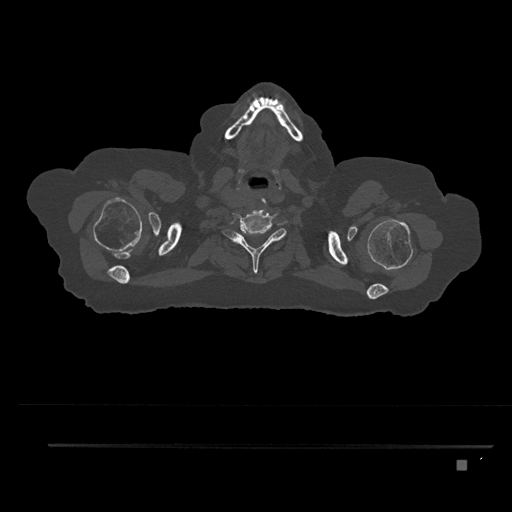
CT including the spine, one axial slice. Position 731 of 797 along the scan axis. Reconstruction kernel Br40s/3. 120 kVp. Bone window (W 1800 / L 400 HU). 0.5 mm slice thickness. 512 × 512 image matrix, field of view 437 × 437 mm. Female patient, age 76 years. Case-level facts recorded for this patient, not image findings: primary cancer: lung; vertebrae with lytic lesions (as recorded): T11, L3.
Outlined on this slice (semi-automatically segmented with operator editing):
- T1 vertebra: bounding box [x1, y1, x2, y2] px = [240, 243, 250, 253]